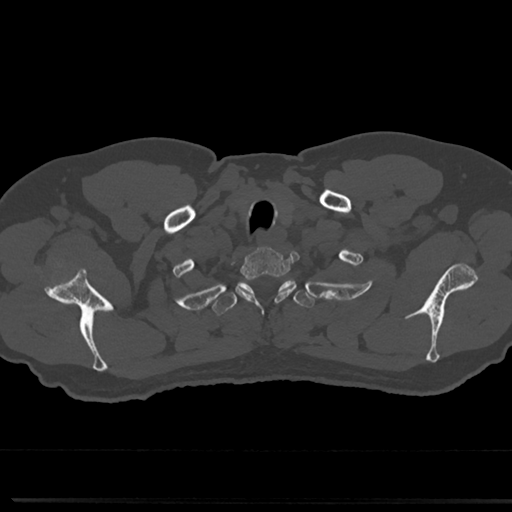
CT including the spine, one axial slice; position 656 of 817 along the scan axis; 120 kVp; bone window (W 1800 / L 400 HU); 0.5 mm slice thickness; 512 × 512 image matrix. Patient: male, 61 years. From the clinical record (not read from this slice): primary cancer: prostate.
Annotated regions visible in this slice (semi-automatic segmentation, software-assisted and operator-edited):
- T1 vertebra: bounding box <238,249,288,300> (left, top, right, bottom; pixels)
- T2 vertebra: <216,276,311,313>